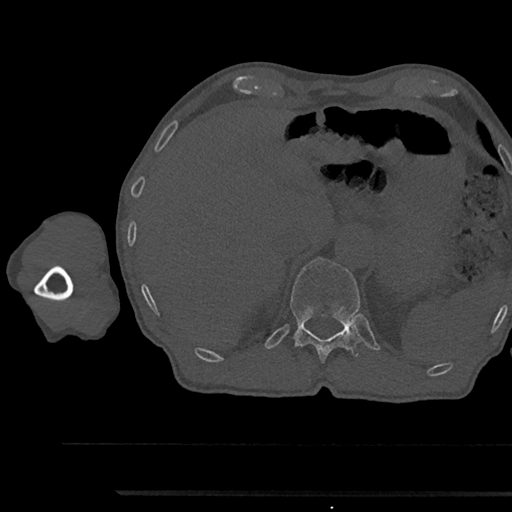
CT including the spine, one axial slice. Slice 714 of 797 in the series (ordered by position). Reconstruction kernel Br40s/3. 120 kVp. Bone window (W 1800 / L 400 HU). 0.5 mm slice thickness. 512 × 512 image matrix, field of view 367 × 367 mm. Patient: male, 79 years. From the clinical record (not read from this slice): primary cancer: prostate.
Annotated regions visible in this slice (semi-automatic segmentation, software-assisted and operator-edited):
- T12 vertebra: bounding box <290,258,363,364> (left, top, right, bottom; pixels)